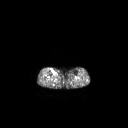
FDG PET of an extremity soft-tissue mass (from a PET/CT study), one axial slice. Slice 131 of 267 in the series (ordered by position). 128 × 128 image matrix. Patient: female, 65 years. Case-level facts recorded for this patient, not image findings: histological type: undifferentiated – high grade; grade: high; site of the primary tumour: right thigh.
Outlined on this slice (expert contour drawn on MRI and transferred to this co-registered scan by the dataset authors):
- gross tumour volume (mass): box from (x=51, y=69) to (x=55, y=73) px